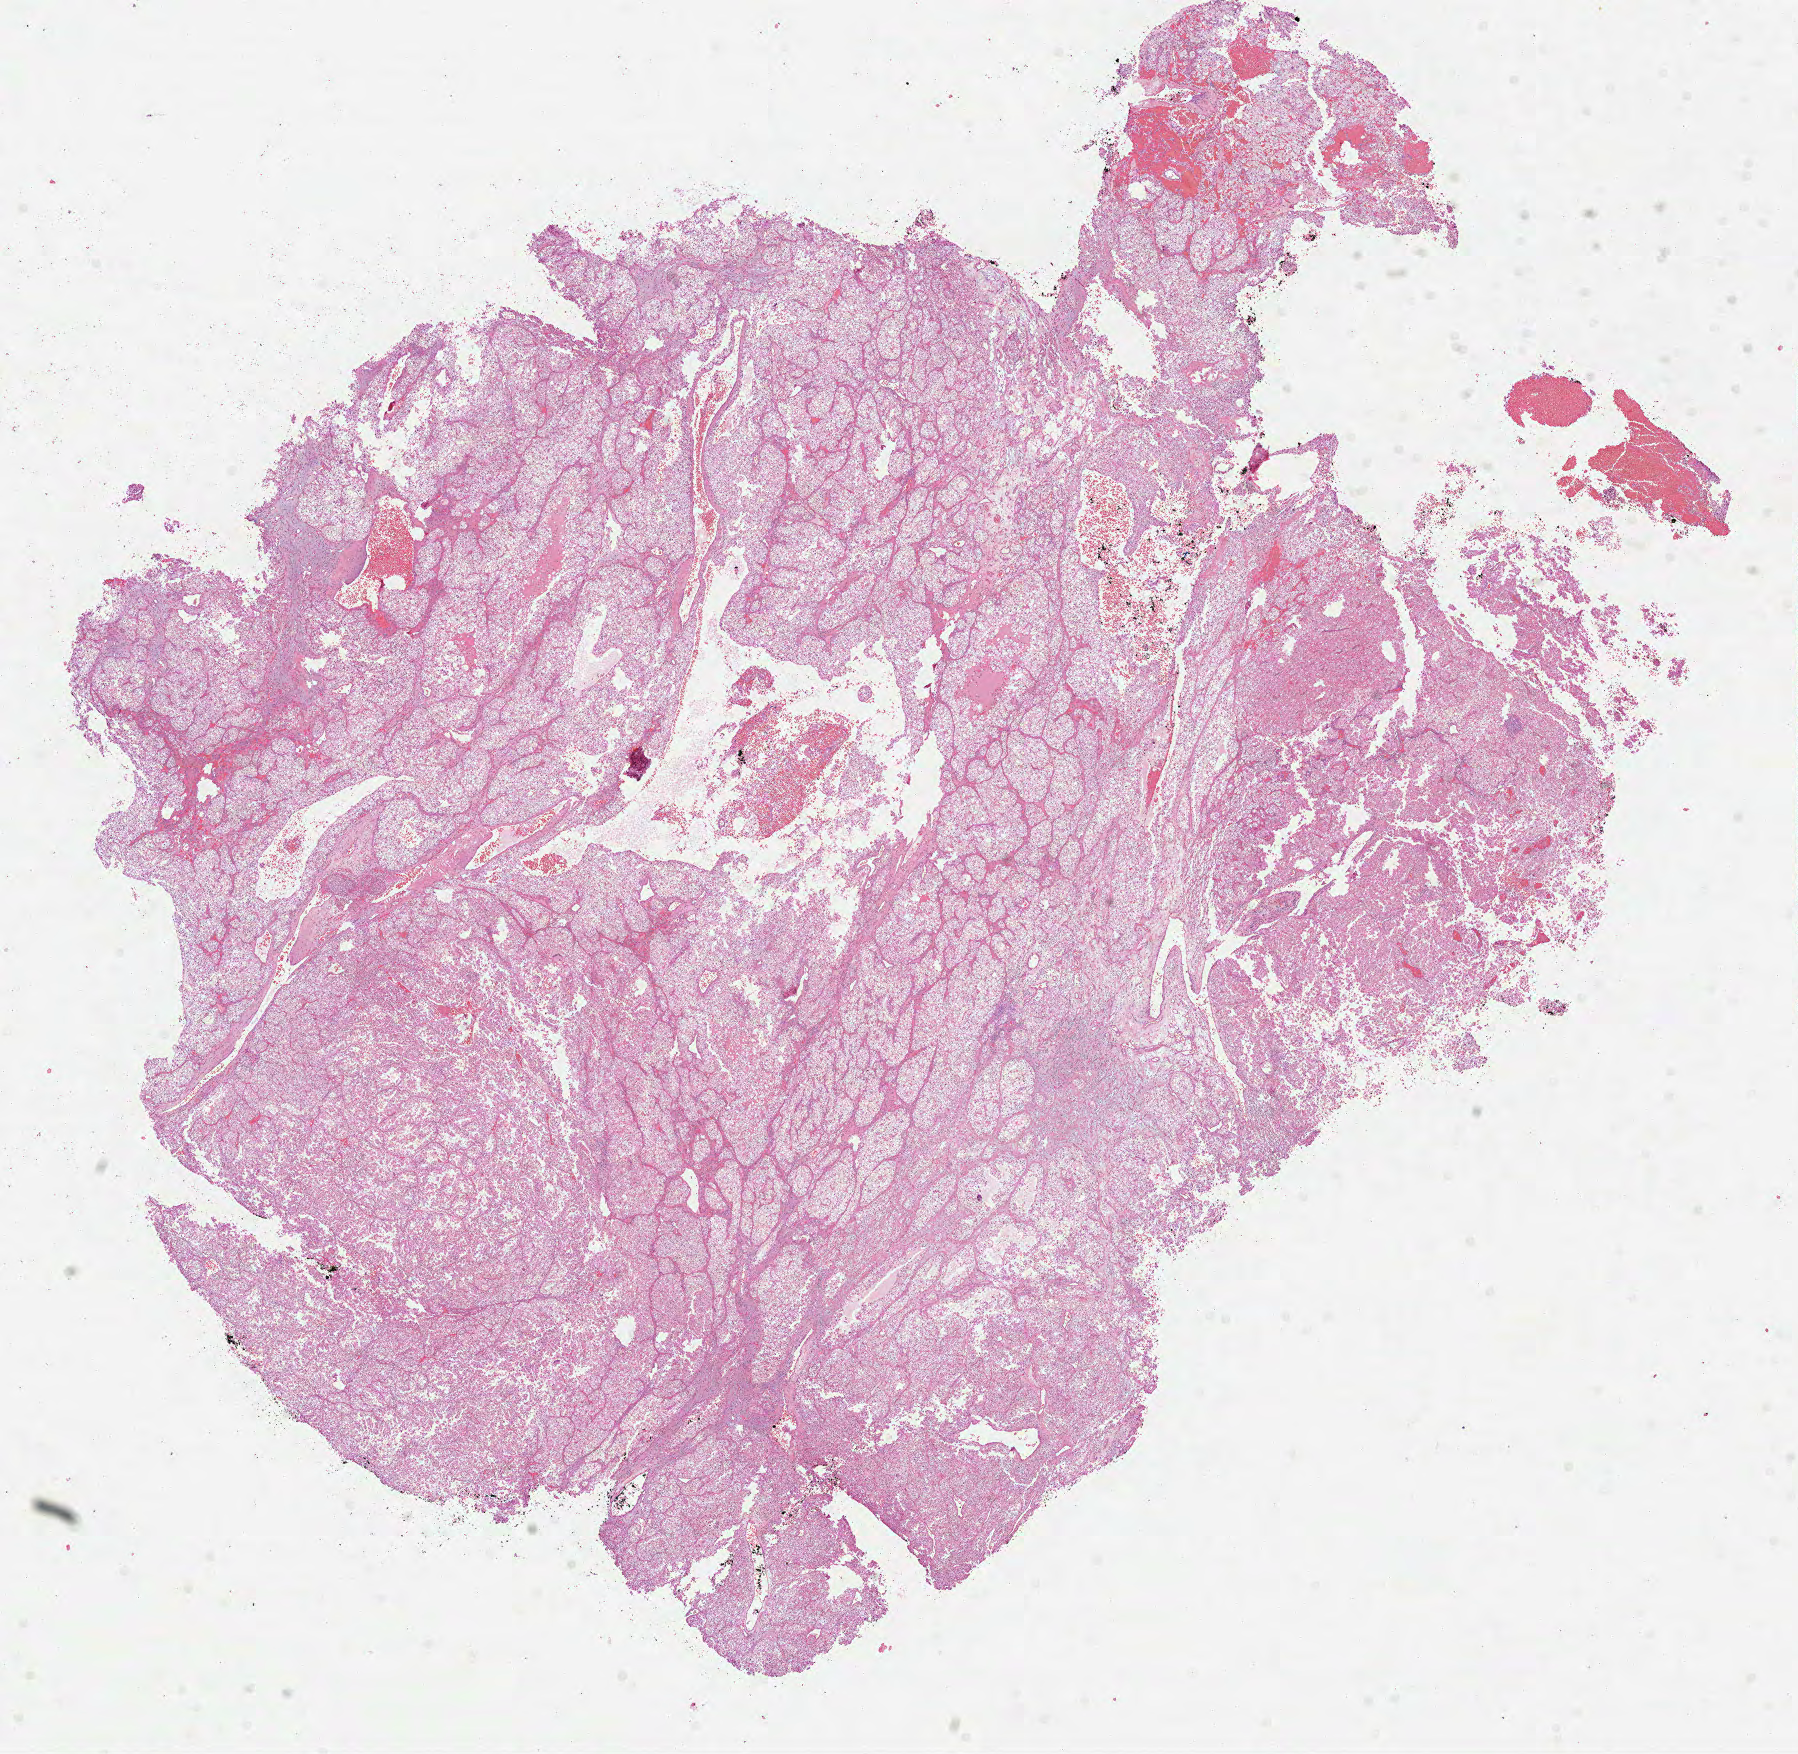
Digitized H&E-stained tissue section (whole slide) — a low-resolution overview of the entire scanned area, about 14.5 x 14.1 mm, formalin-fixed paraffin-embedded (FFPE) diagnostic section, kidney, primary tumour sample. Patient: male, age at initial diagnosis 41 years. Histologic grade: G4 (undifferentiated).
* diagnosis: Clear cell adenocarcinoma, NOS
* AJCC pathologic stage: II